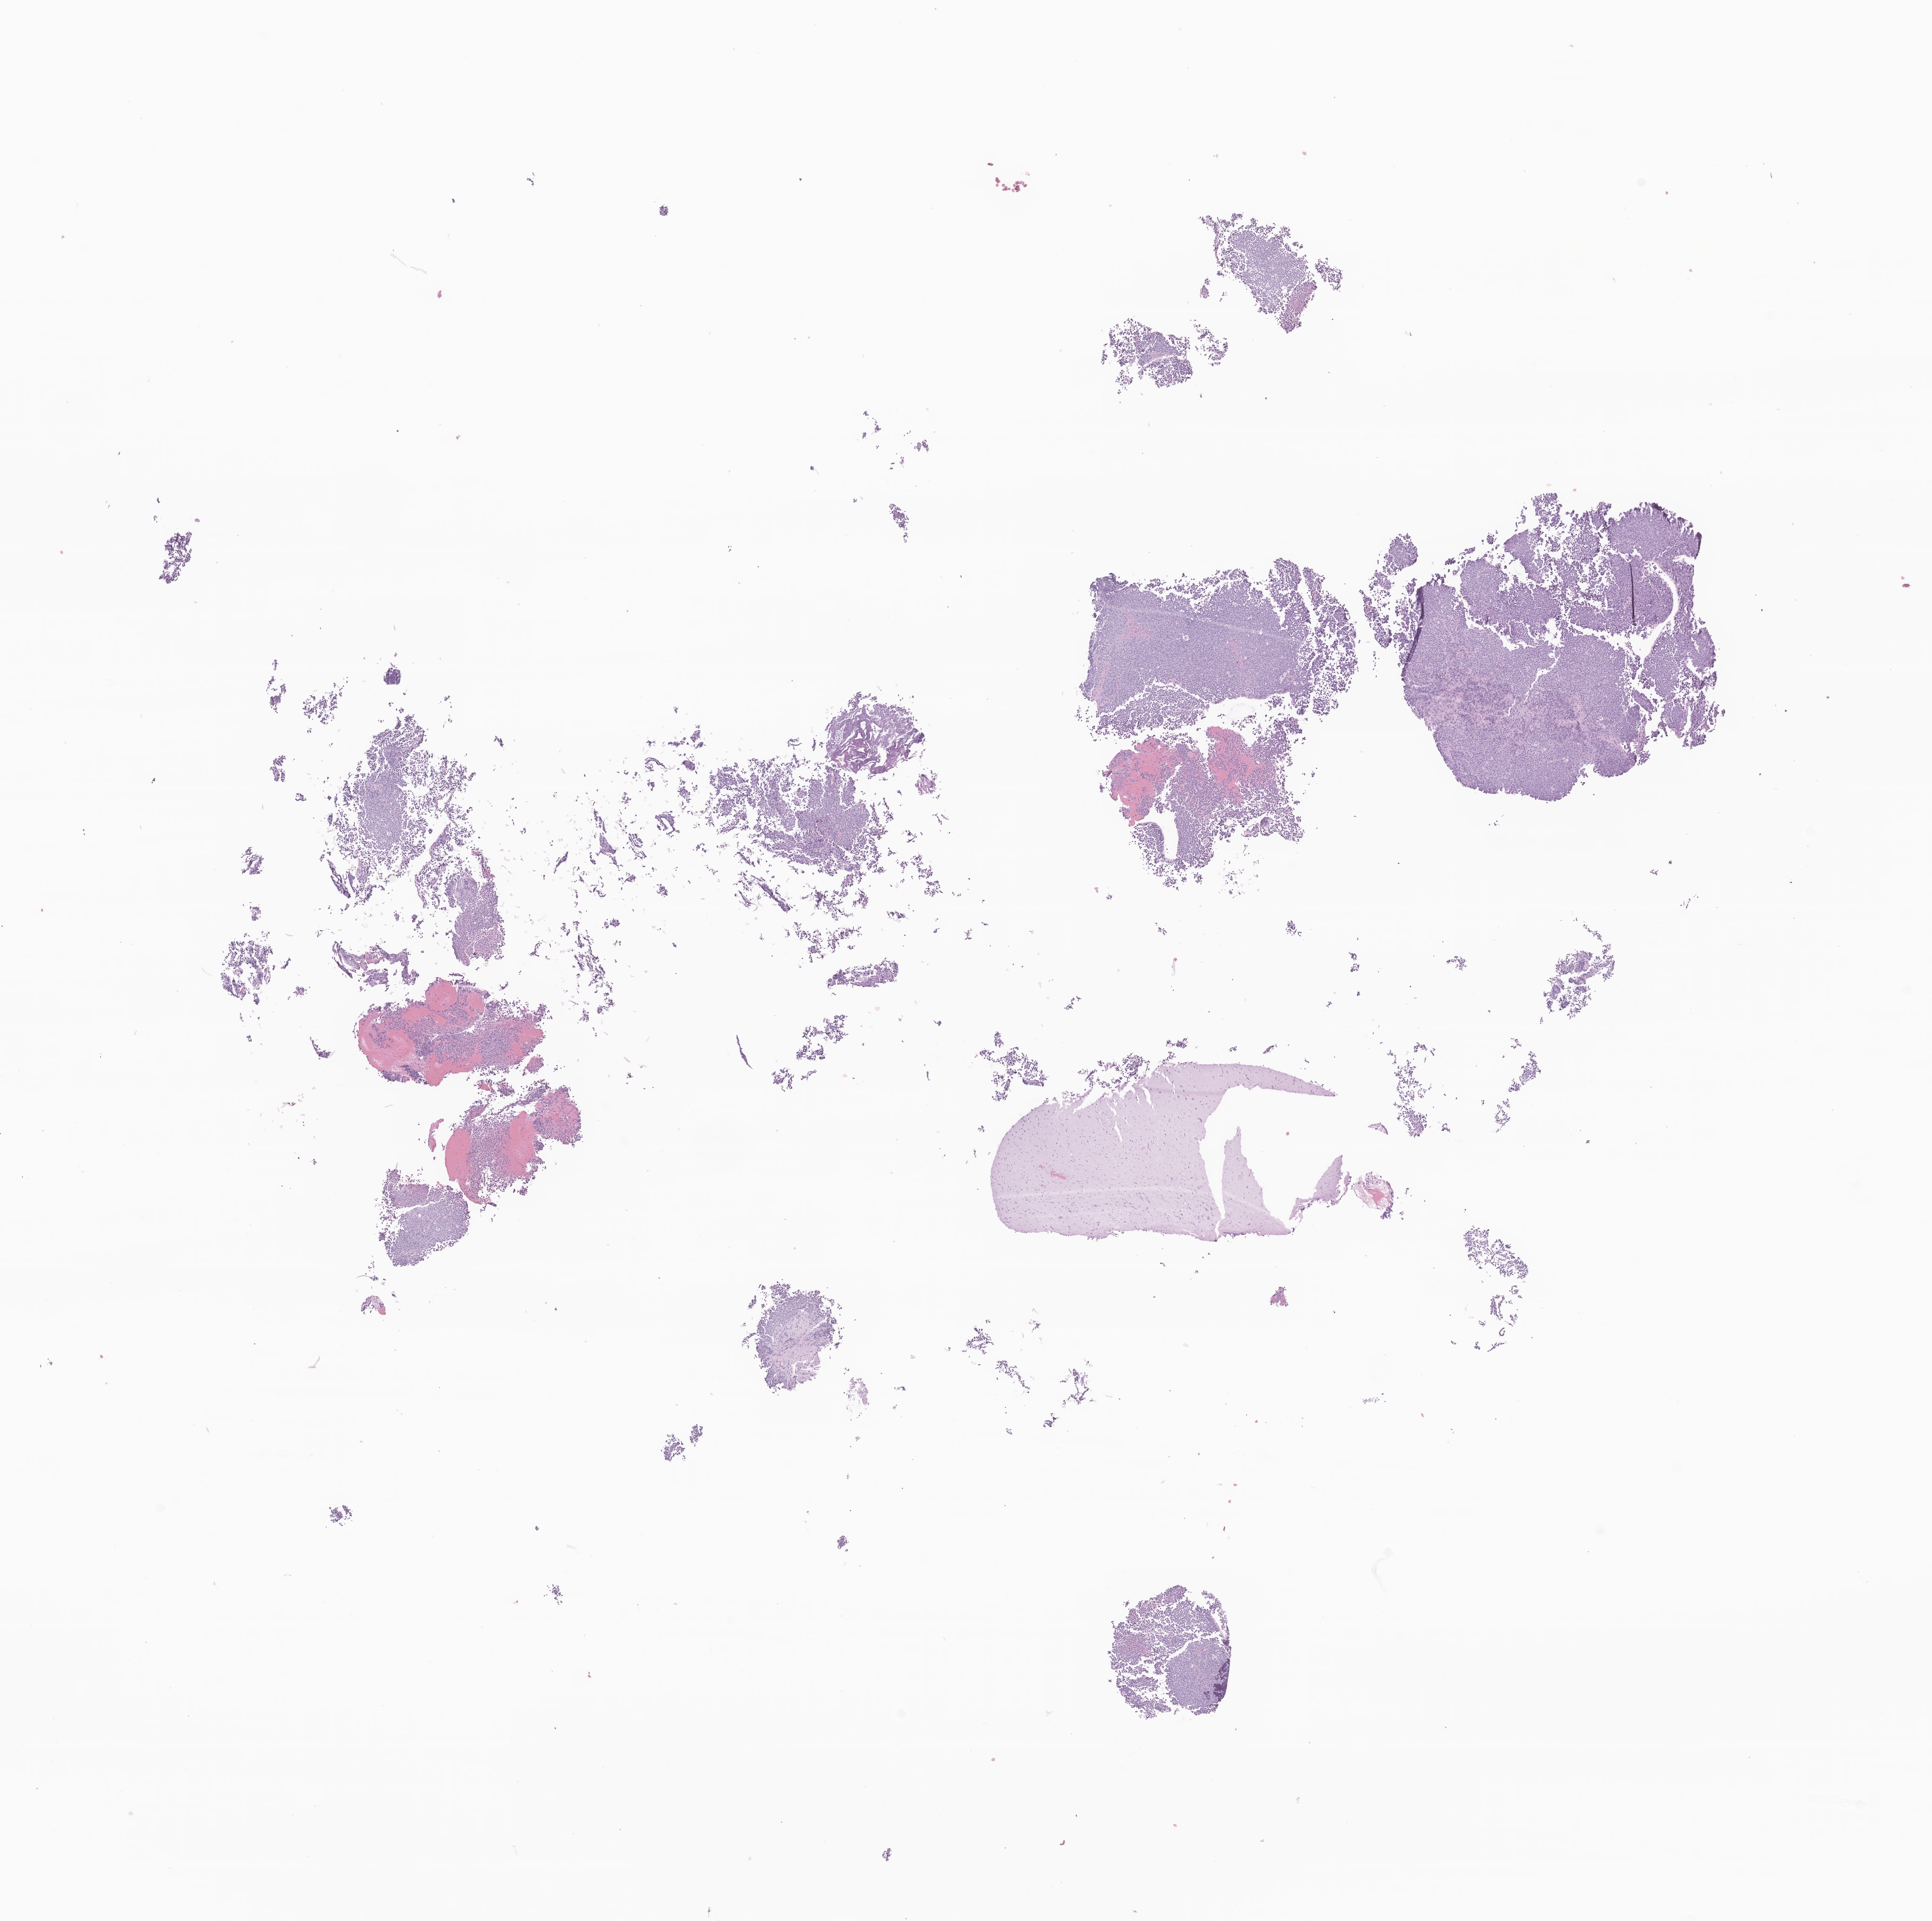
H&E whole-slide image of tumor tissue from the brain, shown as a low-resolution overview of the whole scanned area (about 17.3 x 17.1 mm). FFPE section. Patient male; age 209 months (17 years 5 months).
• recorded diagnosis: Germinoma